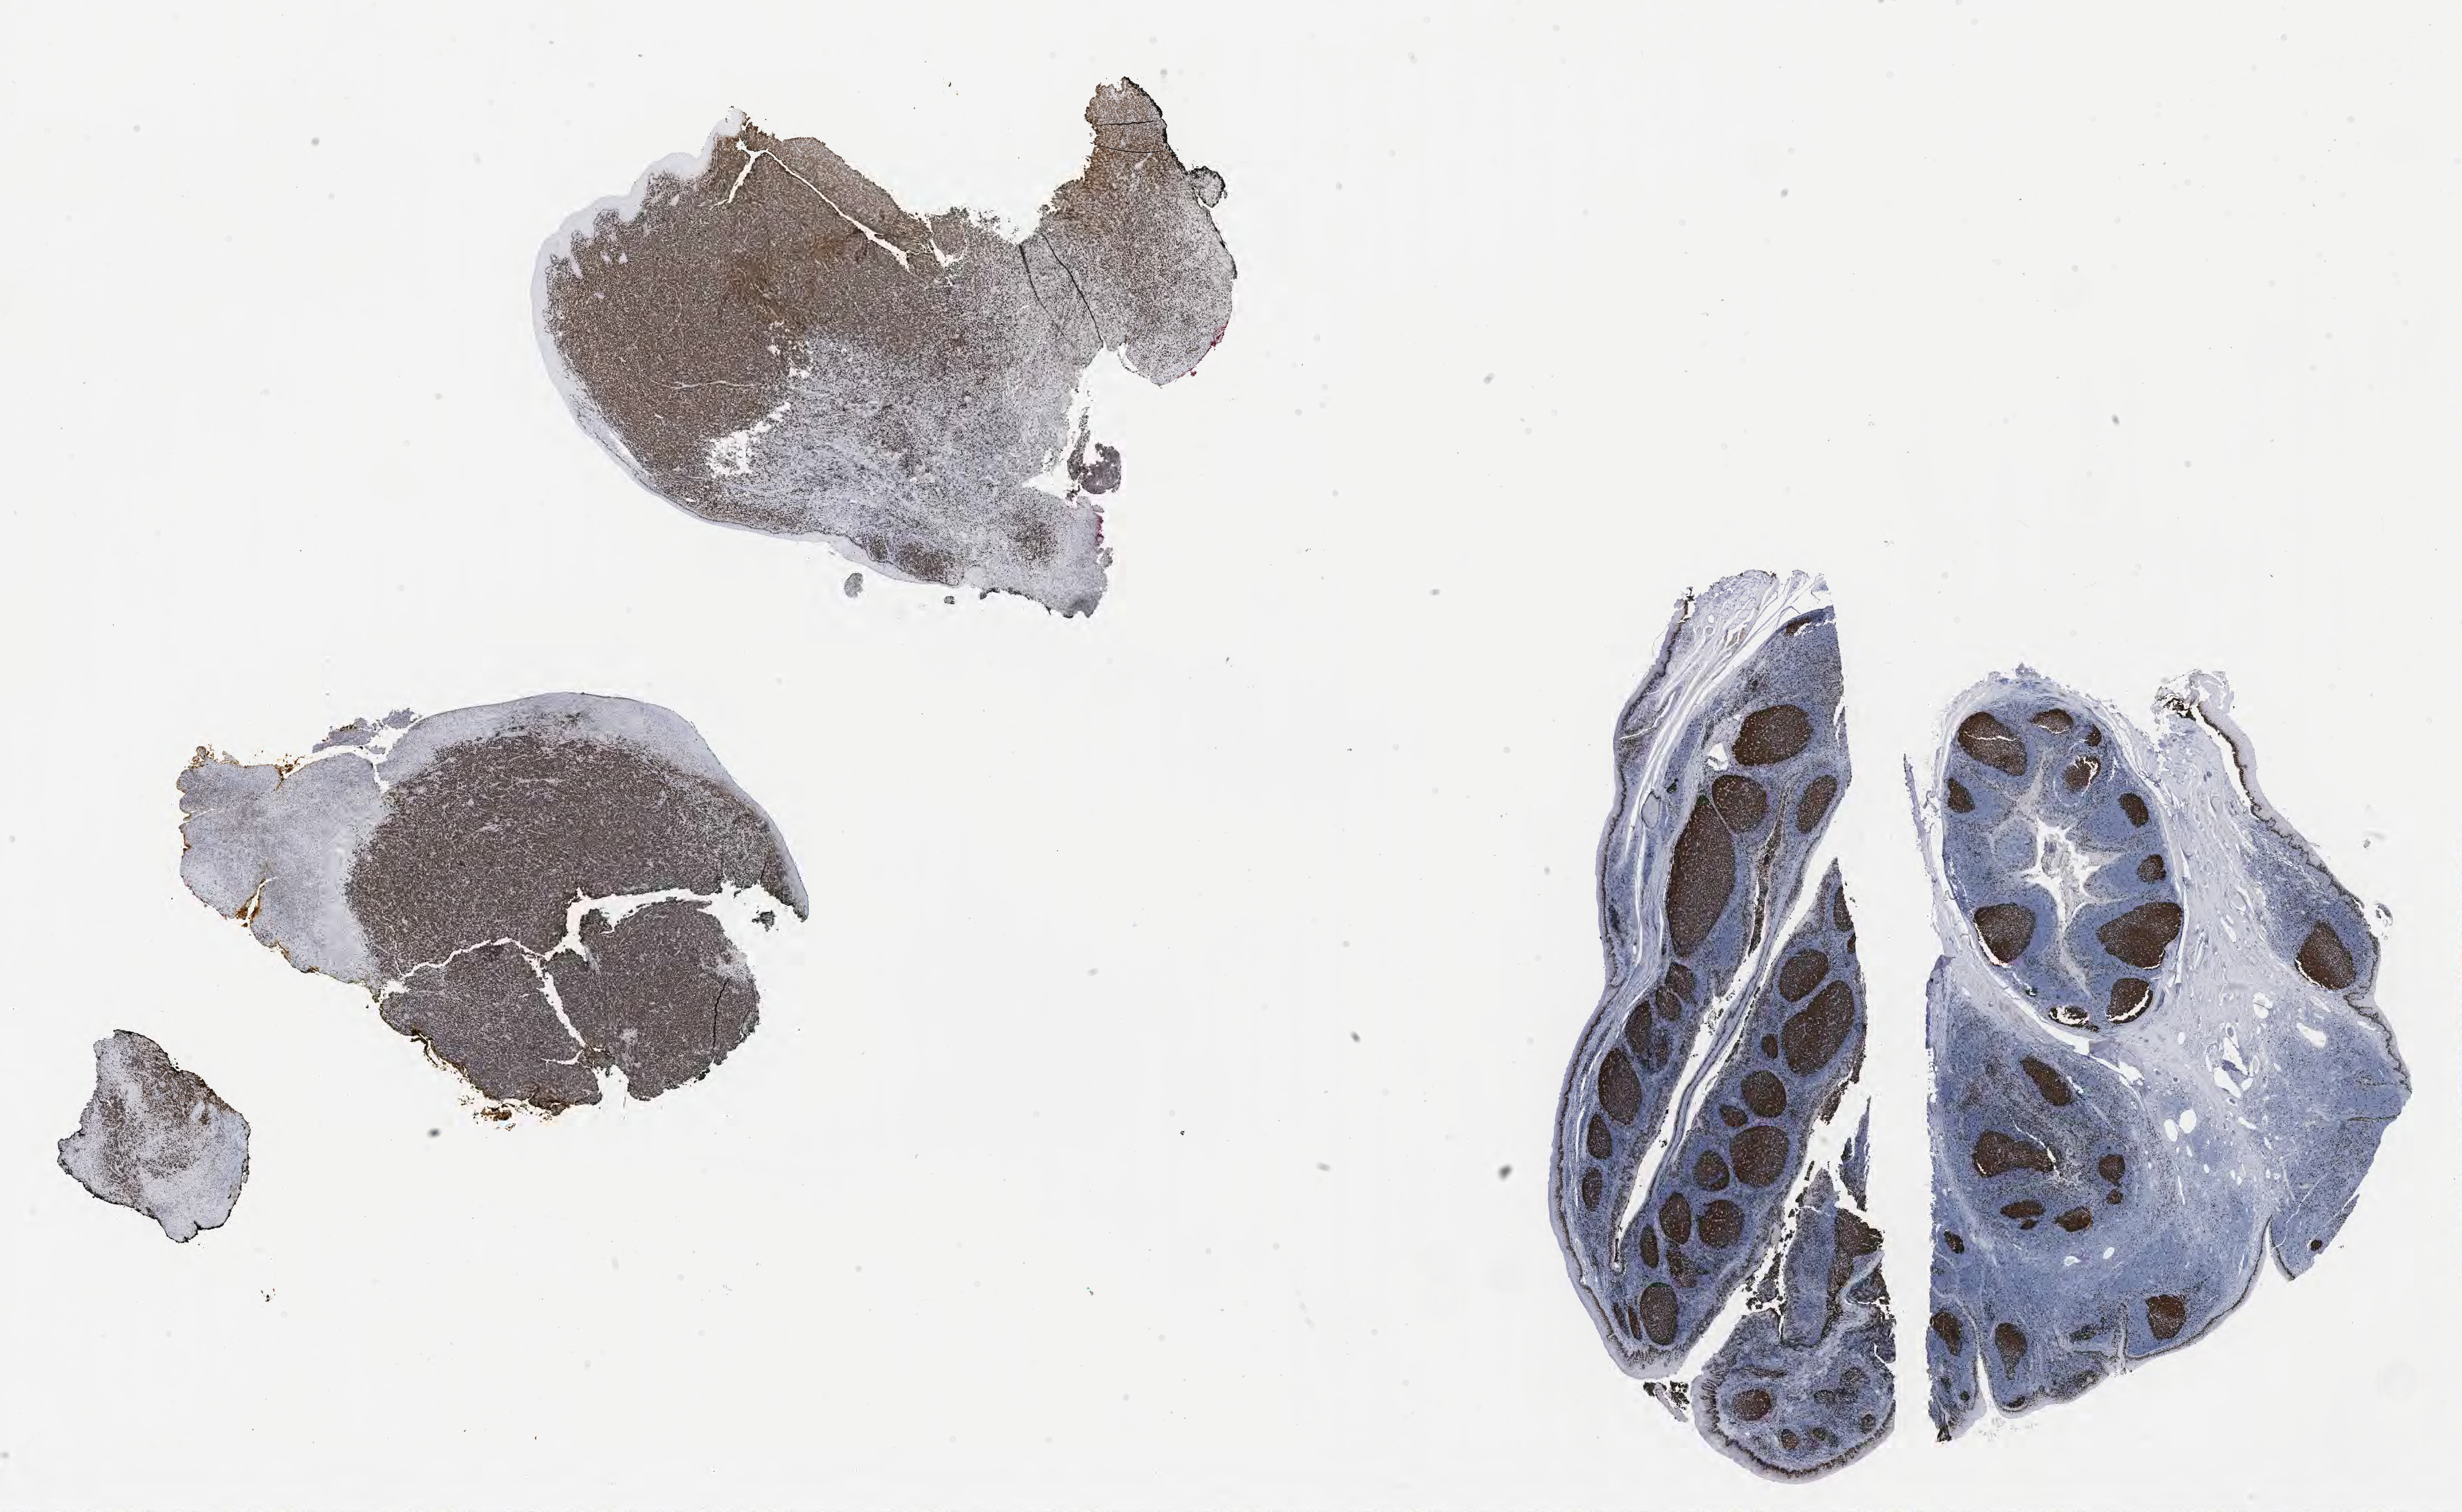
IHC for Ki-67, whole-slide image, whole scanned area (about 29.7 x 18.2 mm) shown as a low-resolution overview. Specimen: tumor tissue. Patient: male, 49 years old.
Histologic diagnosis: Diffuse large B-cell lymphoma, NOS.